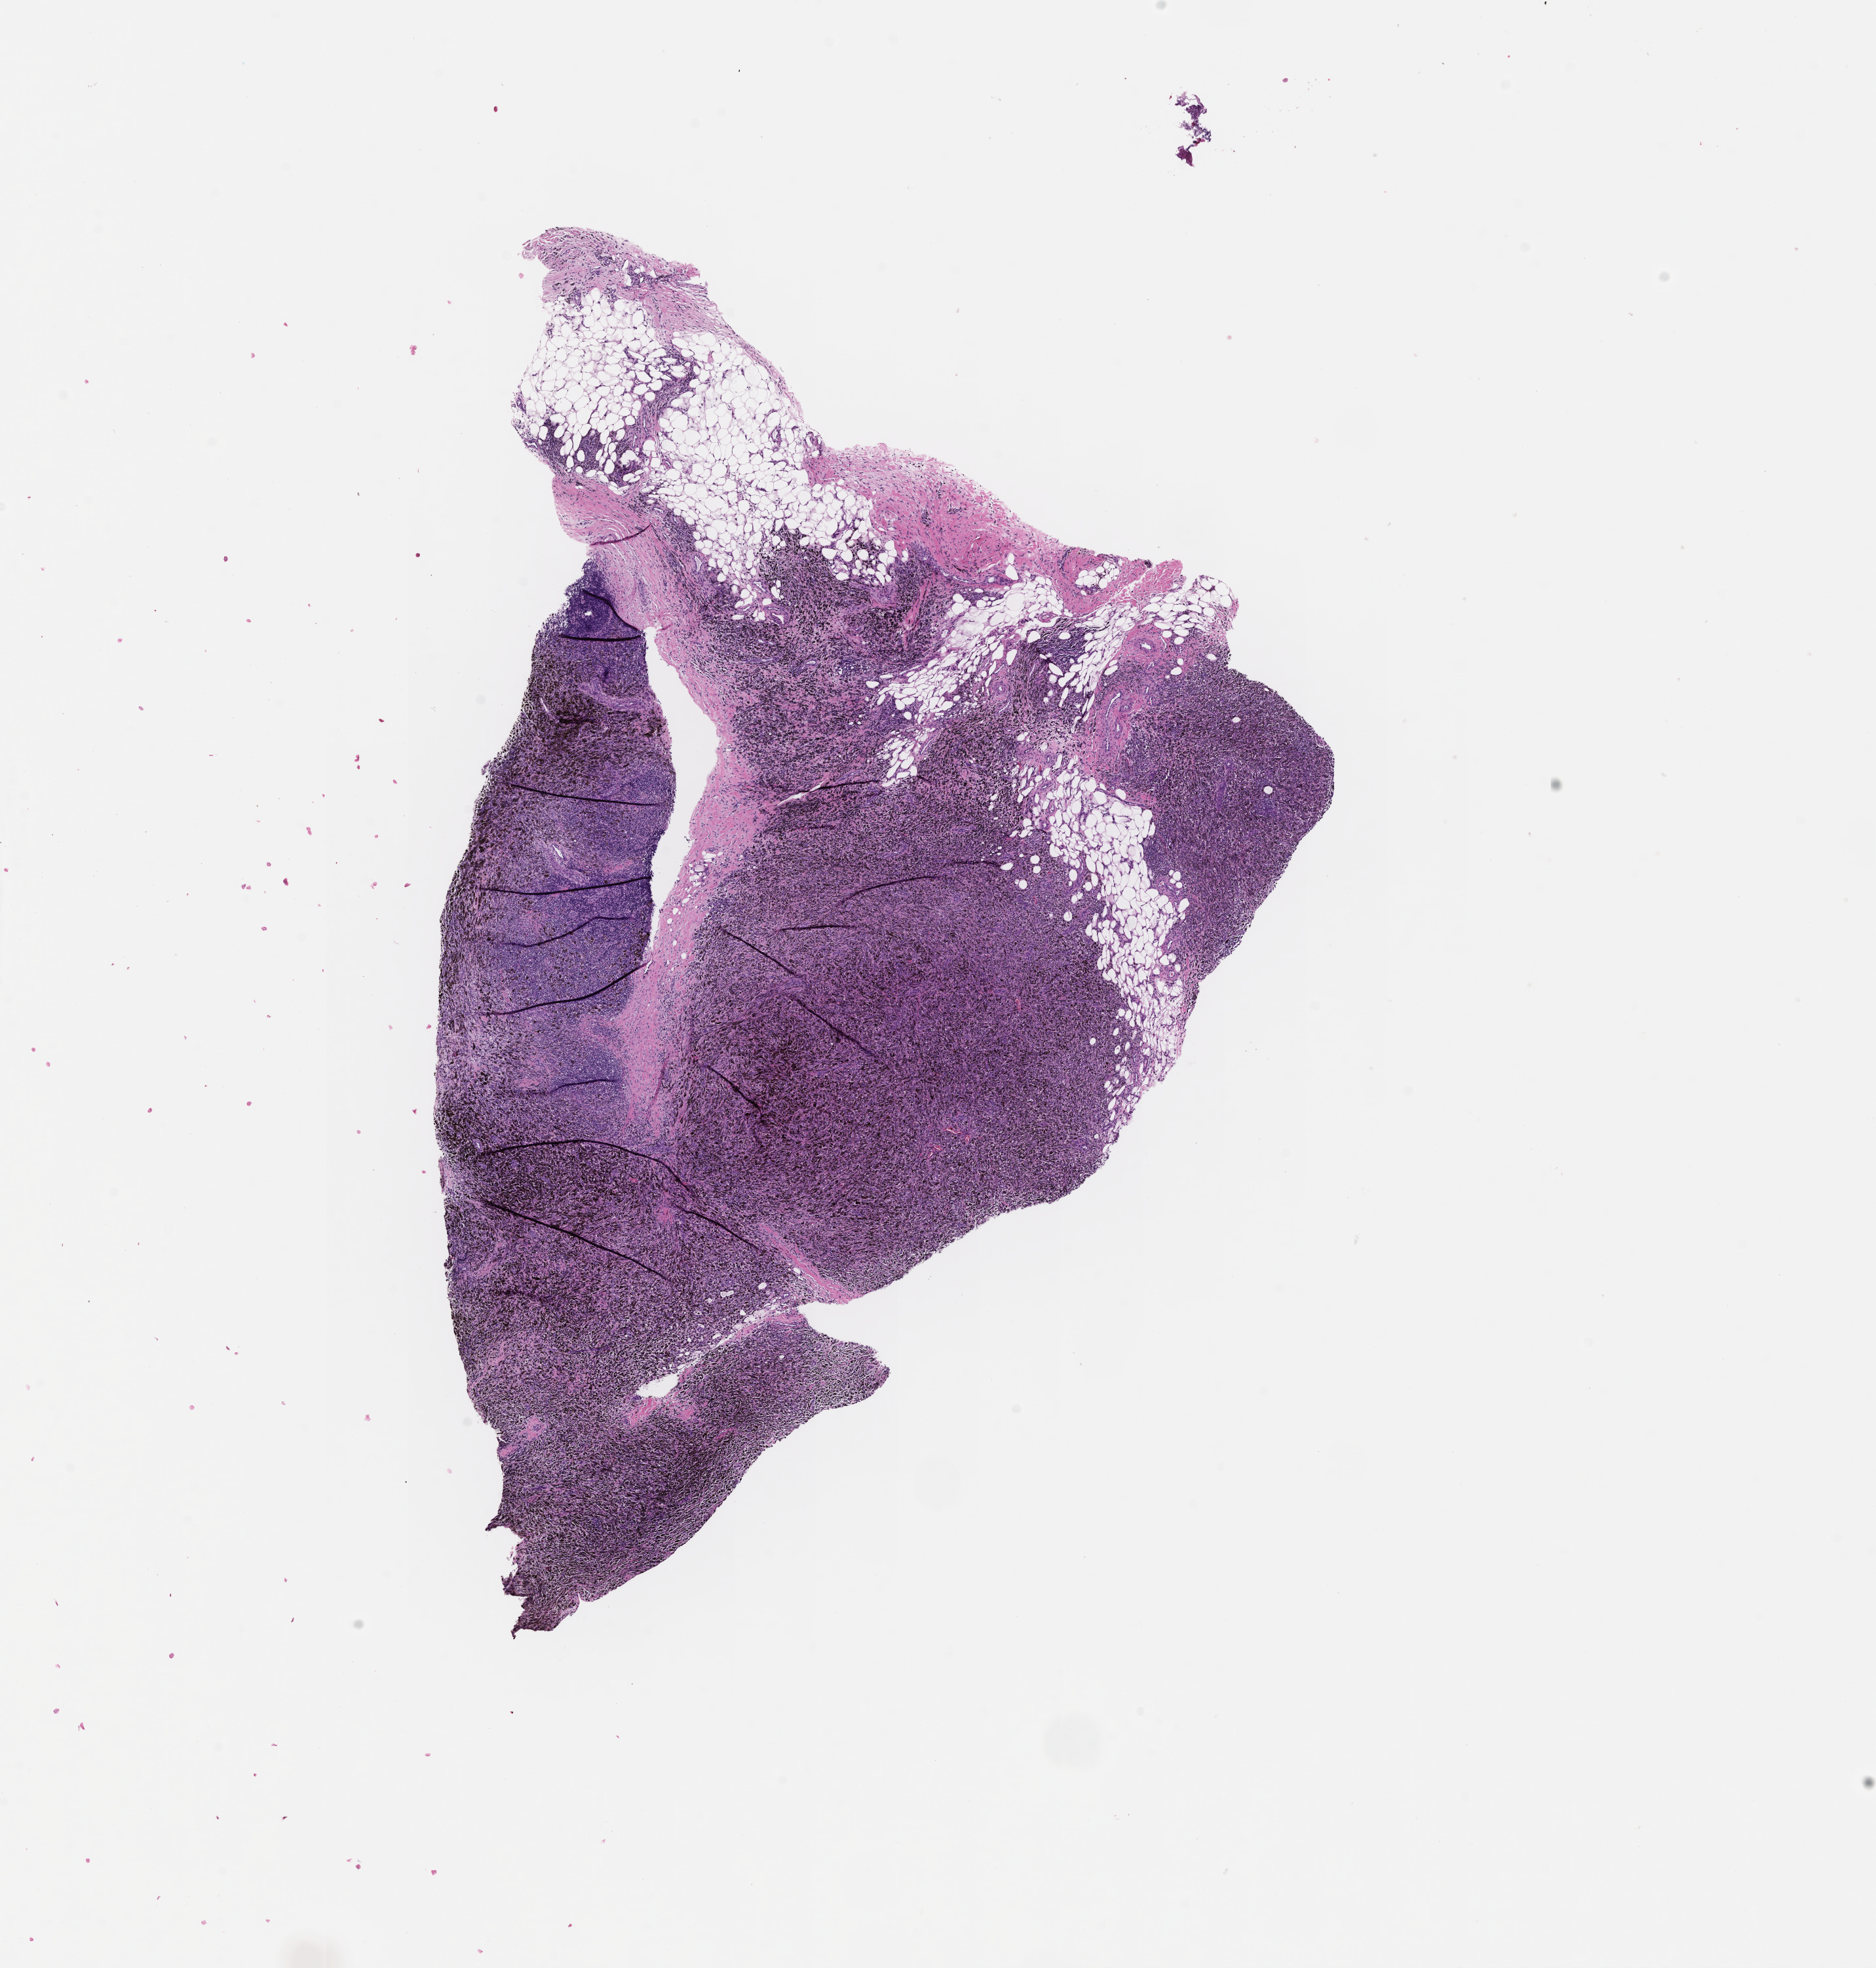
Digitized hematoxylin and eosin (H&E)-stained section, whole scanned area (about 11.6 x 12.1 mm) shown as a low-resolution overview. Formalin-fixed paraffin-embedded section. Site: skin. Specimen time point: collected at disease progression. Male patient.
This section: primary tumour tissue. Diagnosis: Melanoma.